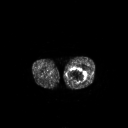
FDG PET of an extremity soft-tissue mass (from a PET/CT study), one axial slice; position 233 of 267 along the scan axis; 128 × 128 image matrix. Patient: male, 44 years. Case-level facts recorded for this patient, not image findings: histological type: undifferentiated pleomorphic liposarcoma; grade: high; site of the primary tumour: left thigh.
Annotated regions visible in this slice (expert contour drawn on MRI and transferred to this co-registered scan by the dataset authors):
- gross tumour volume including surrounding oedema: bounding box [x1, y1, x2, y2] px = [67, 67, 87, 83]
- gross tumour volume (mass): [67, 67, 87, 83]